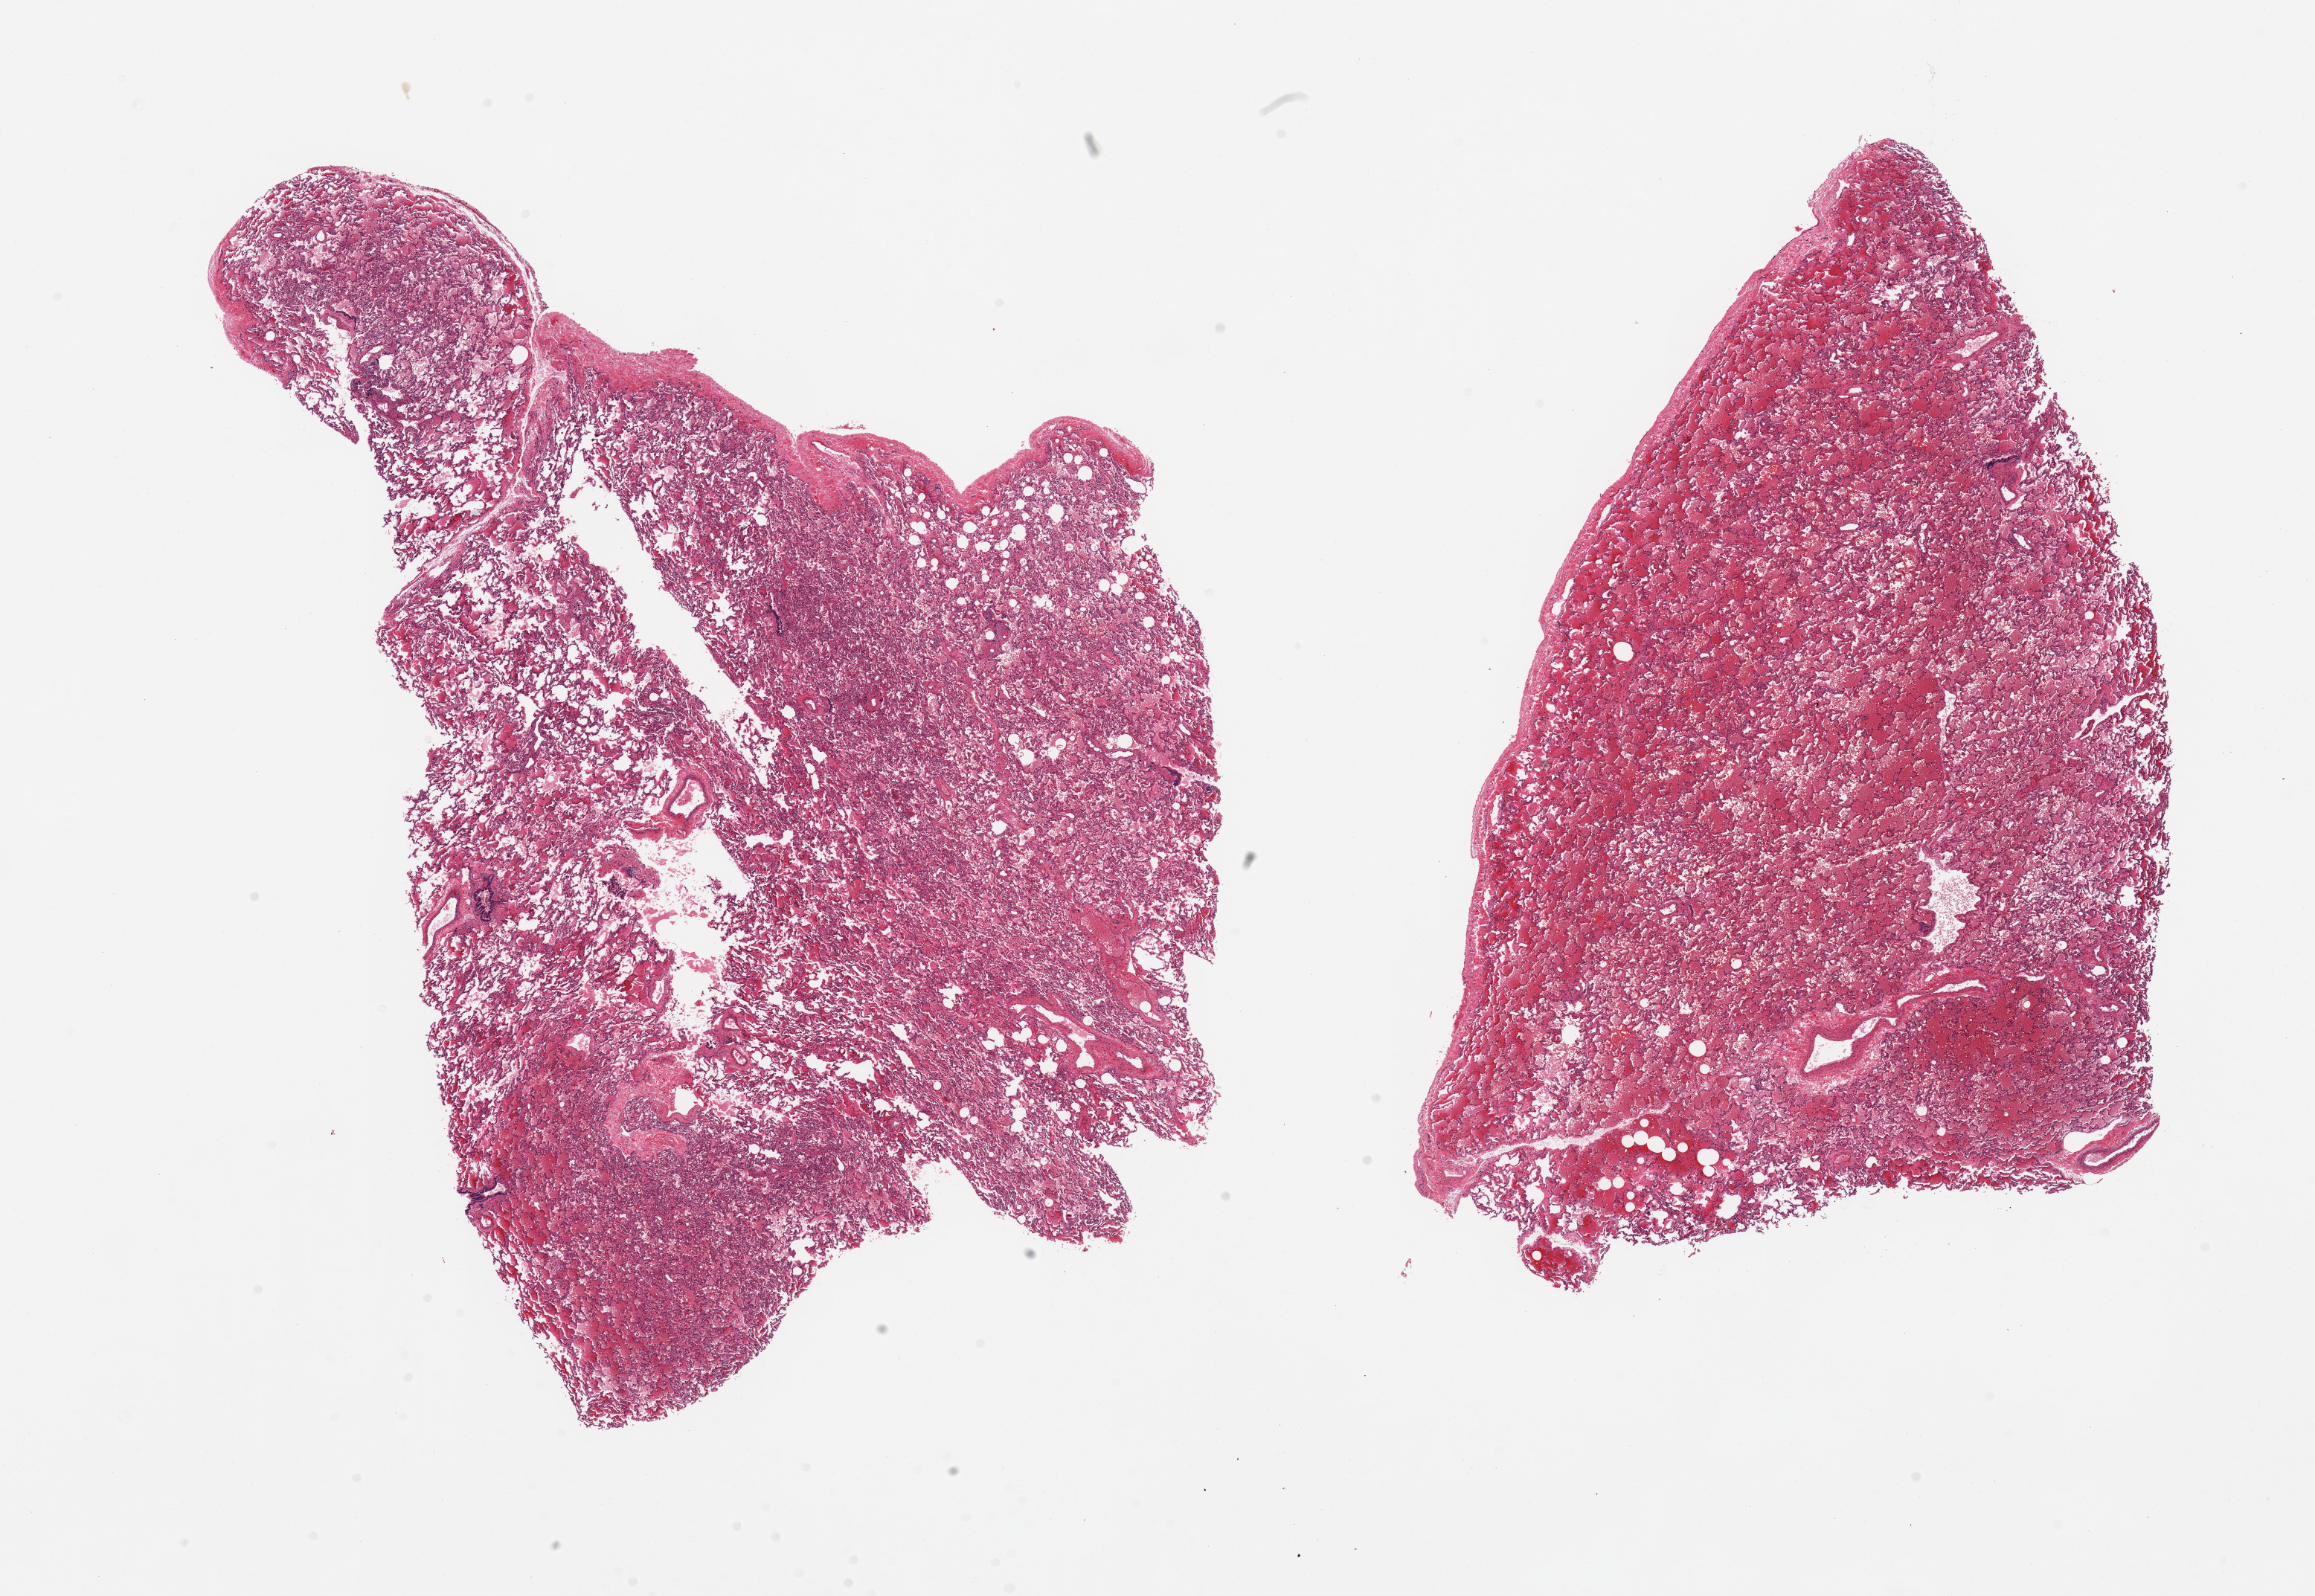
Whole-slide image, haematoxylin and eosin stain — shown as a low-resolution overview of the whole scanned area (about 24.6 x 17.0 mm, slide scanned at 20x). PAXgene-fixed, paraffin-embedded tissue. Target tissue: lung. Tissue donor sample. Male donor.
Pathologist's review note for this sample: 2 pieces; includes pleura (target is 1cm below pleura), hemorrhage, edema.